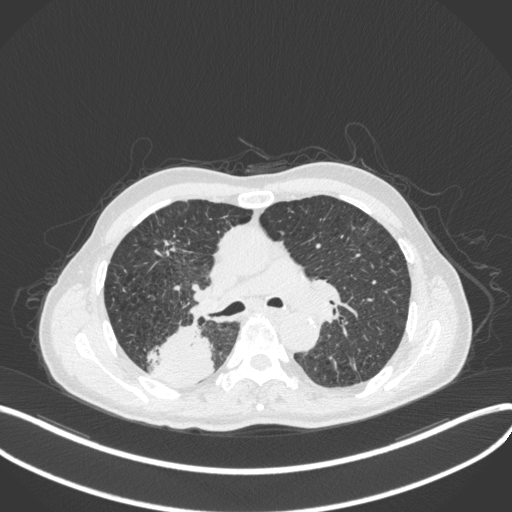
Chest CT, one axial slice. Reconstruction kernel B31f. 120 kVp. Lung window (W 1500 / L -600 HU). 1 mm slice thickness. 512 × 512 image matrix, field of view 400 × 400 mm. Patient: male, 79 years. Case-level facts recorded for this patient, not image findings: clinical TNM (as recorded): T3 N0 M0.
Annotated regions visible in this slice (rectangle marked by the reading radiologist):
- lung tumour (recorded histology: adenocarcinoma): bounding box [x1, y1, x2, y2] px = [147, 320, 217, 389]